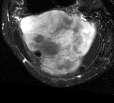
MRI of an extremity soft-tissue mass, one axial slice. Position 26 of 44 along the scan axis. T2-weighted fat-saturated. MR volume resampled by the dataset authors to the PET/CT grid (not the native acquisition matrix). 114 × 103 image matrix, field of view 111 × 101 mm. Female patient. From the clinical record (not read from this slice): histological type: liposarcoma; site of the primary tumour: right thigh.
Annotated regions visible in this slice (expert contour drawn on MRI and transferred to this co-registered scan by the dataset authors):
- gross tumour volume (mass): box from (x=20, y=9) to (x=98, y=76) px